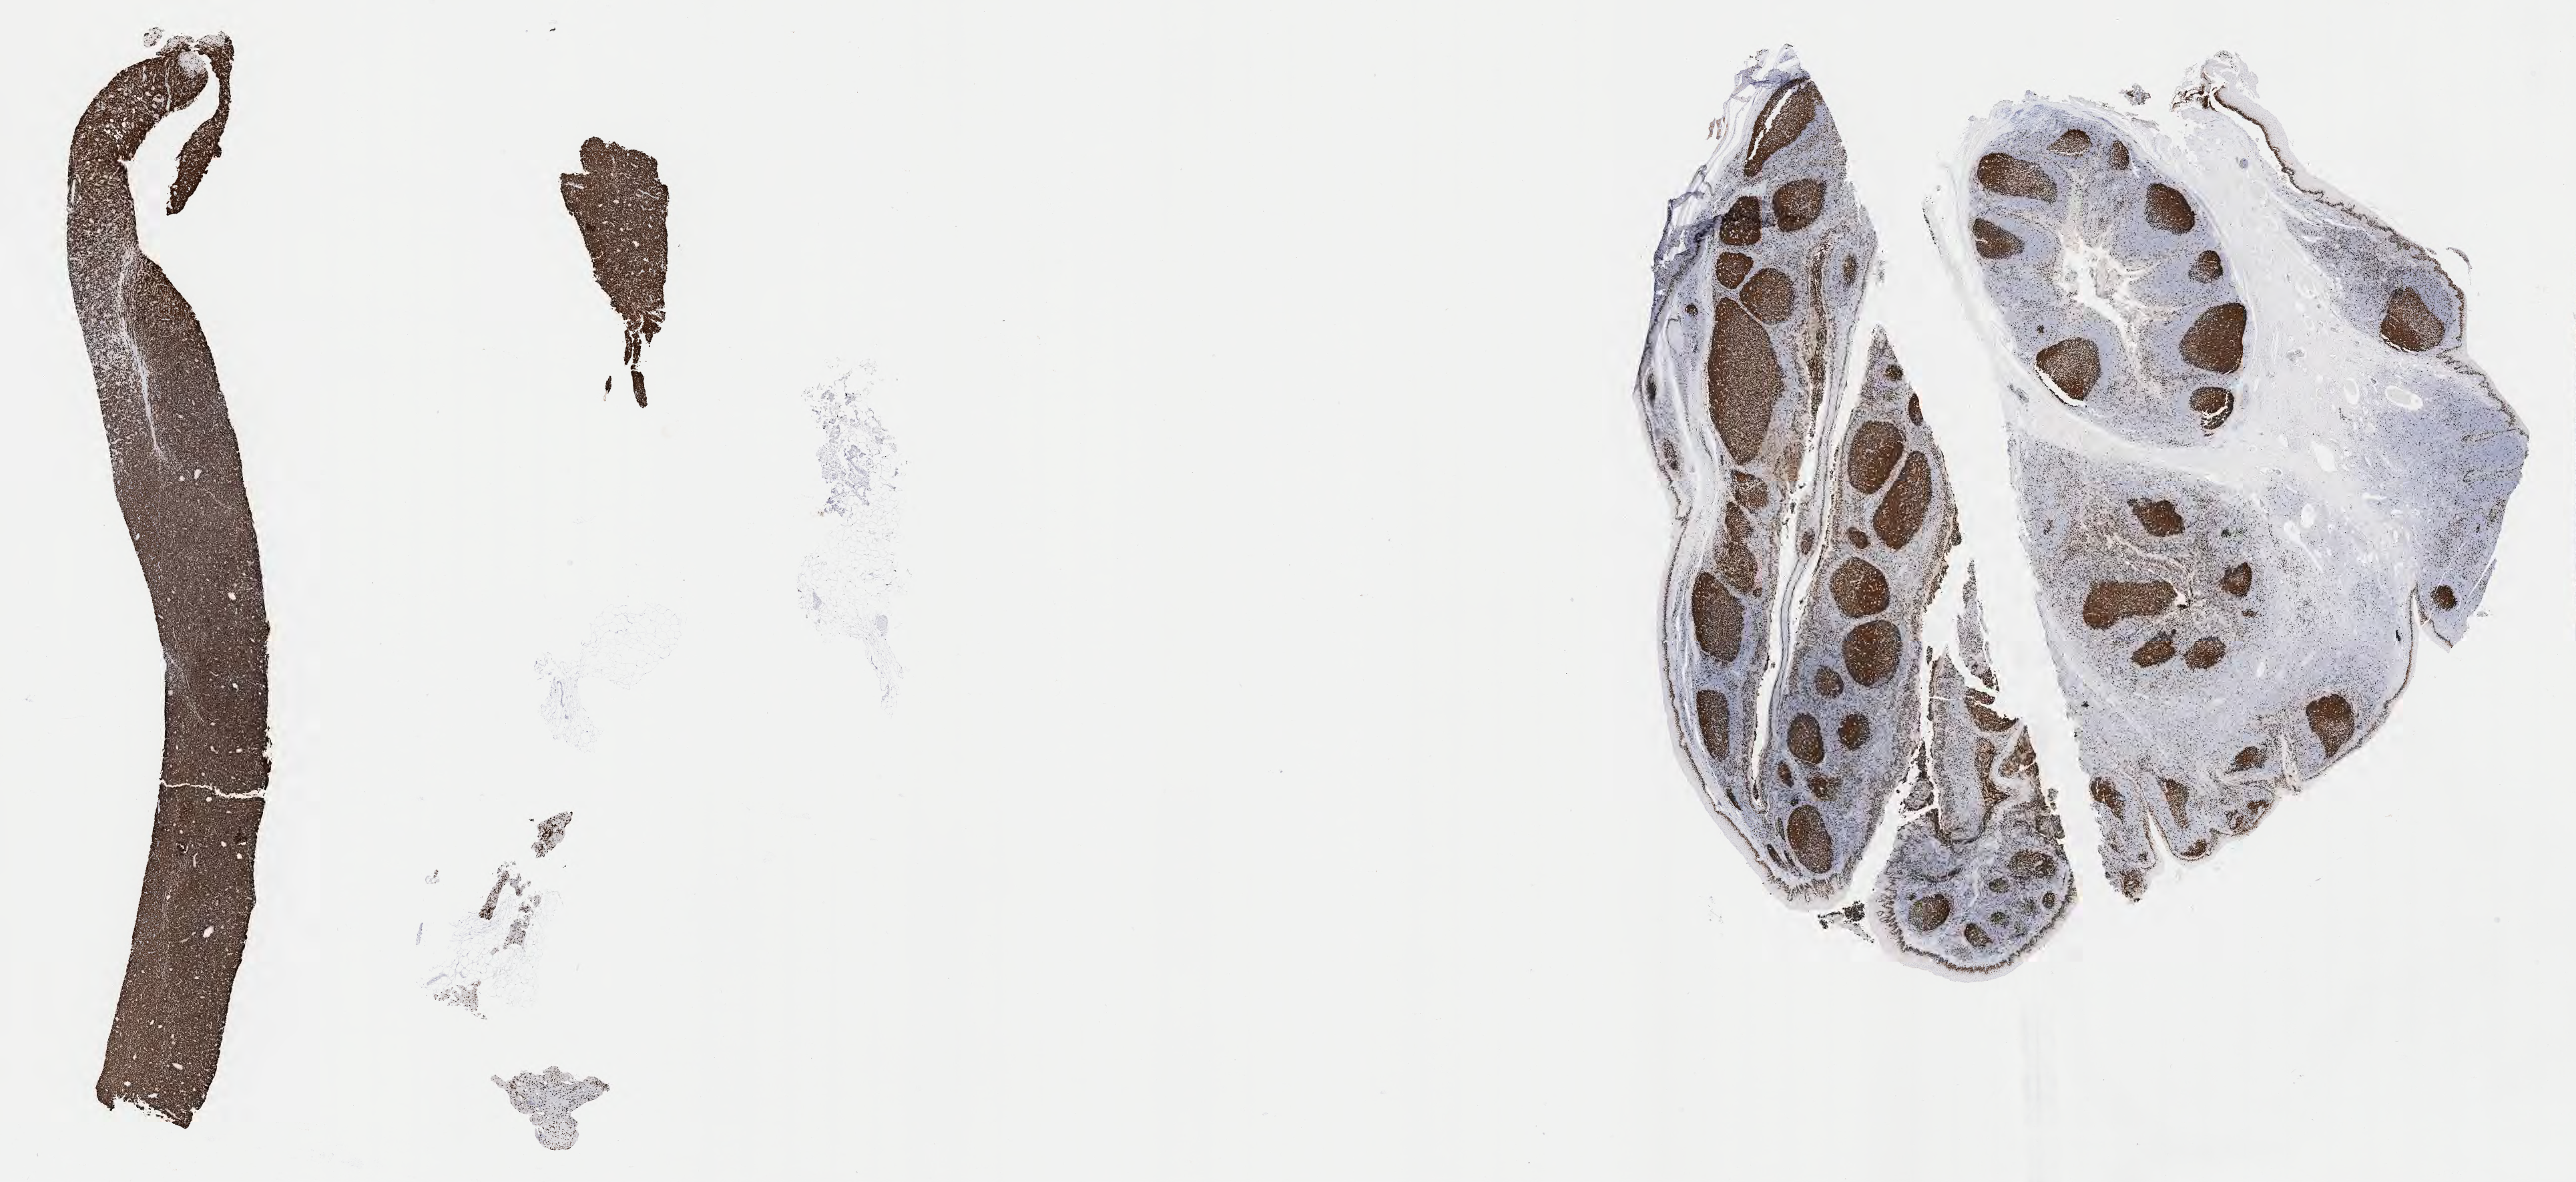
Whole-slide image, immunohistochemical stain for Ki-67, low-resolution overview of the scanned area, about 31.2 x 14.3 mm. Specimen: tumor tissue. Female patient, aged 61.
Histologic diagnosis: Burkitt lymphoma, NOS.